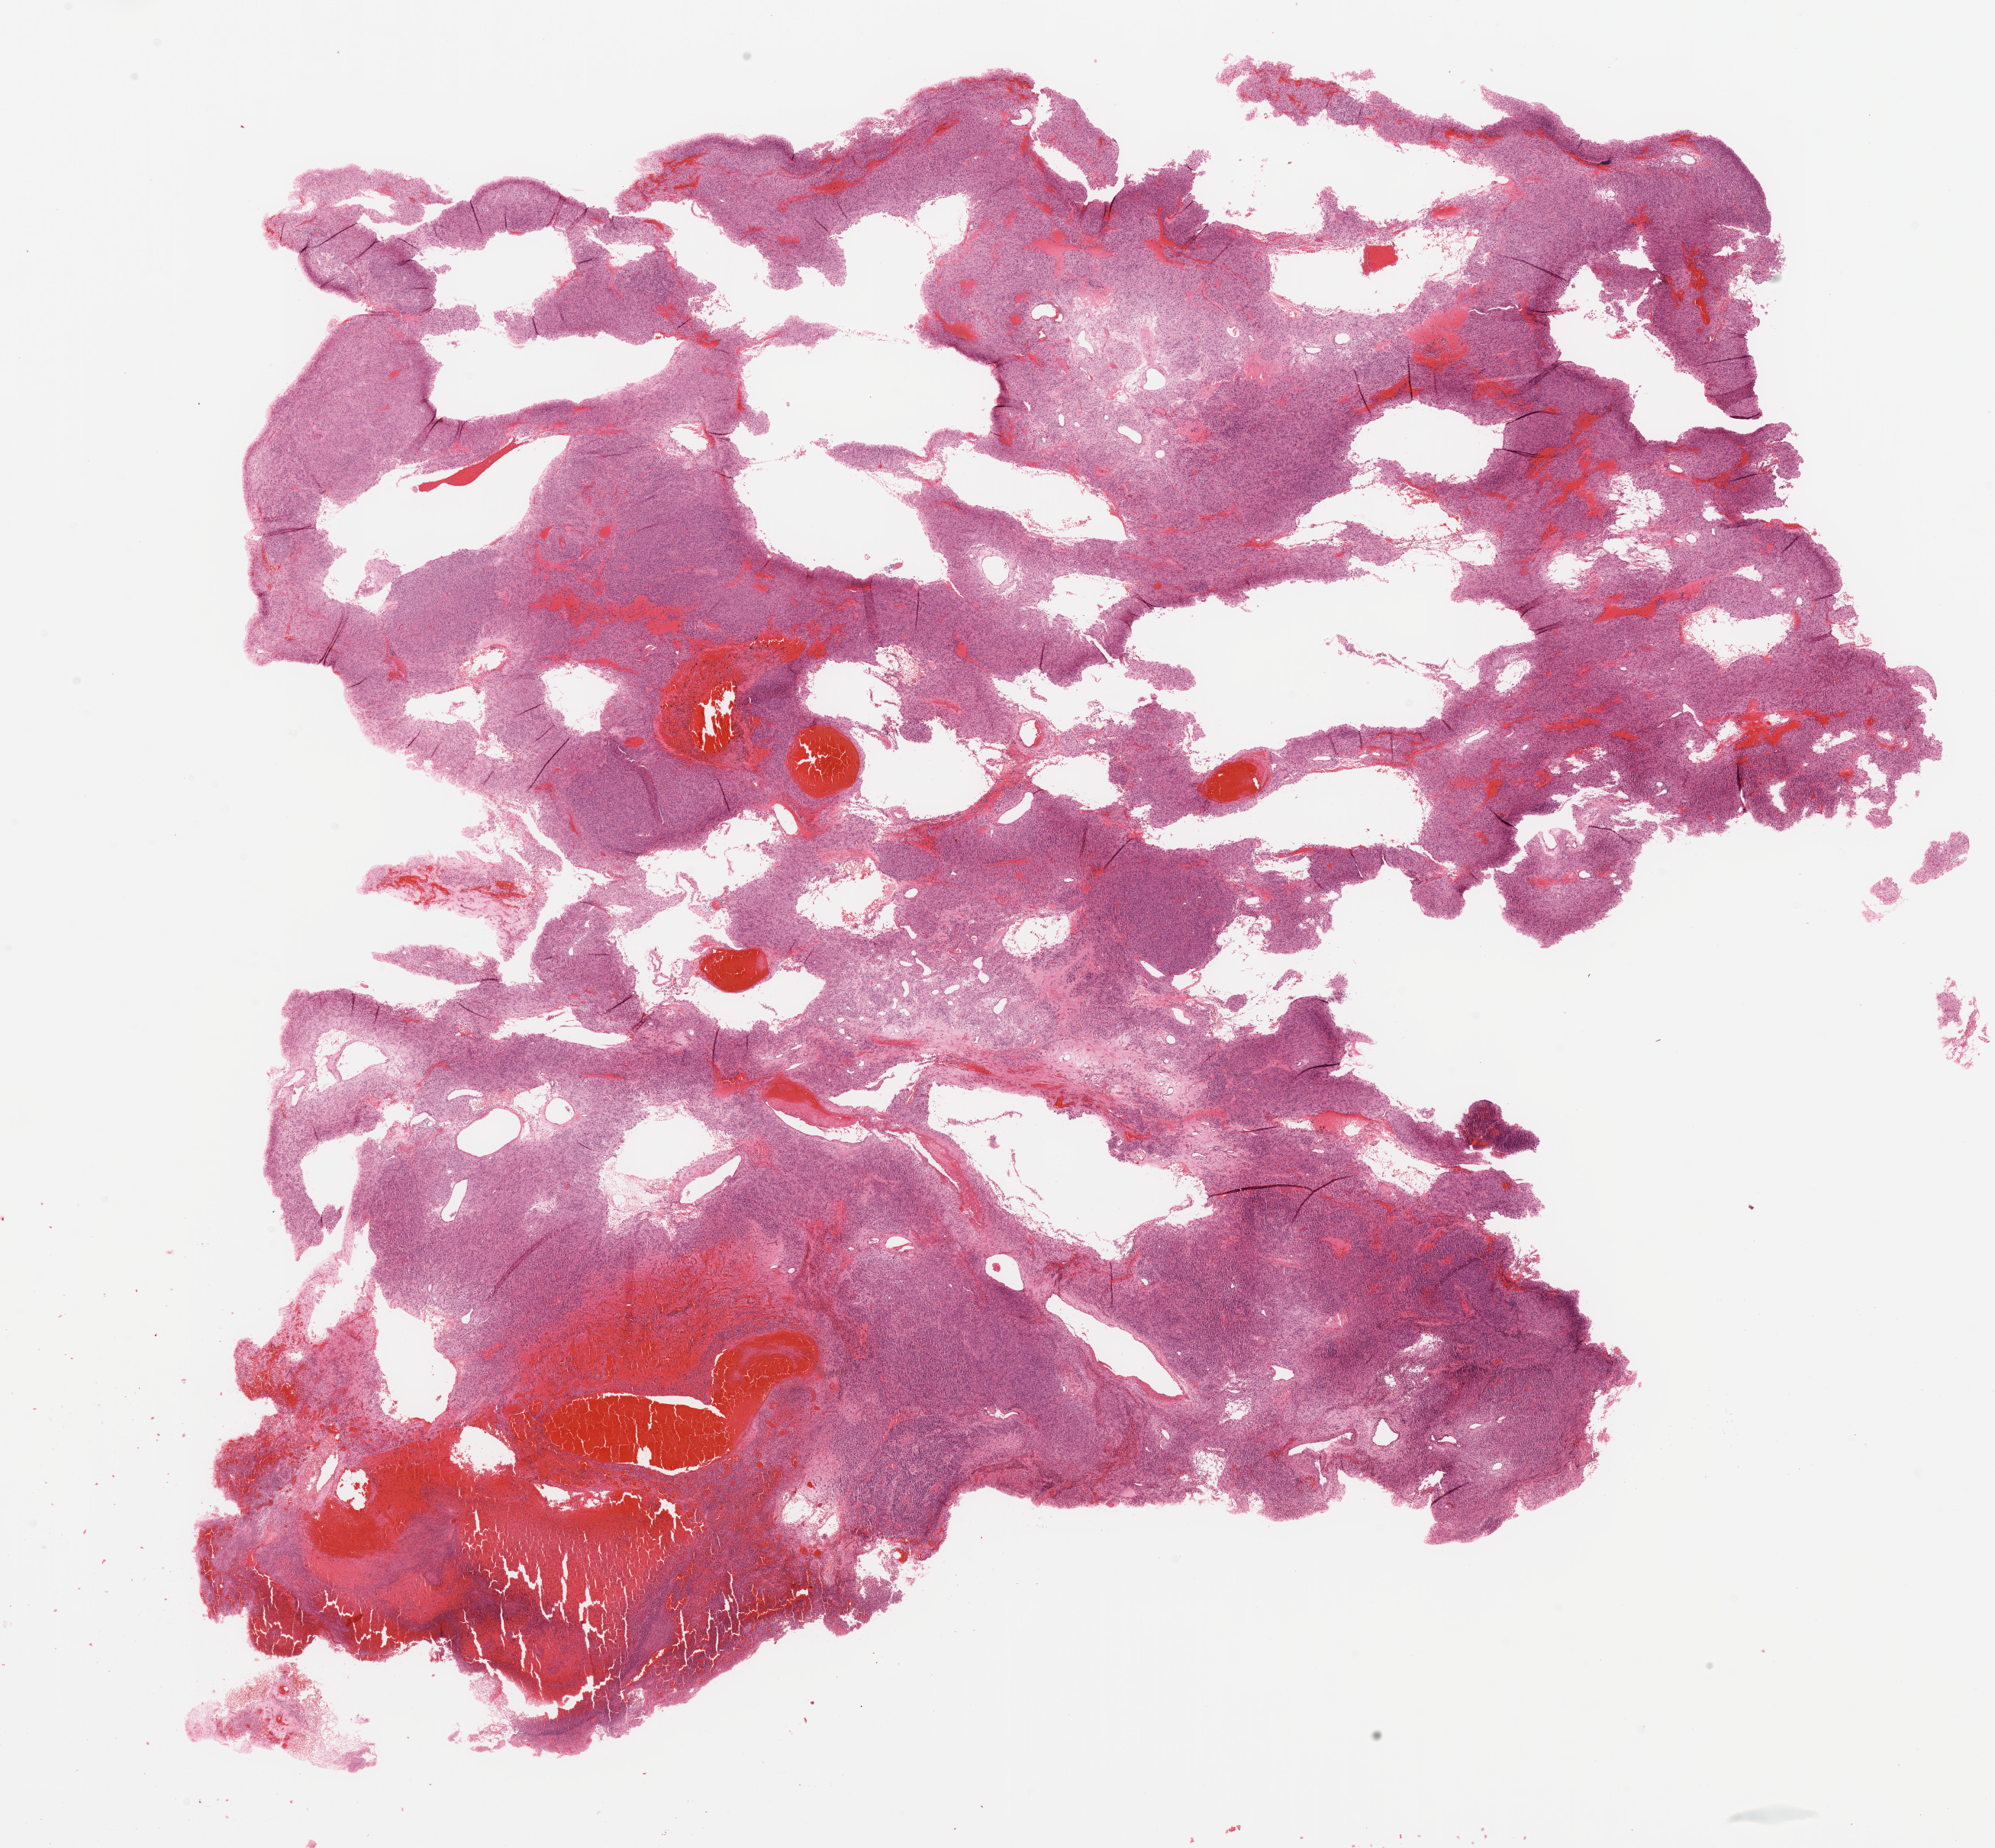
Whole-slide histology image, H&E-stained, low-resolution overview of the scanned area, about 20.7 x 19.2 mm (slide scanned at 20x). 73-year-old female patient.
• patient diagnosis (cohort enrolment): sarcoma (site not recorded at cohort level)